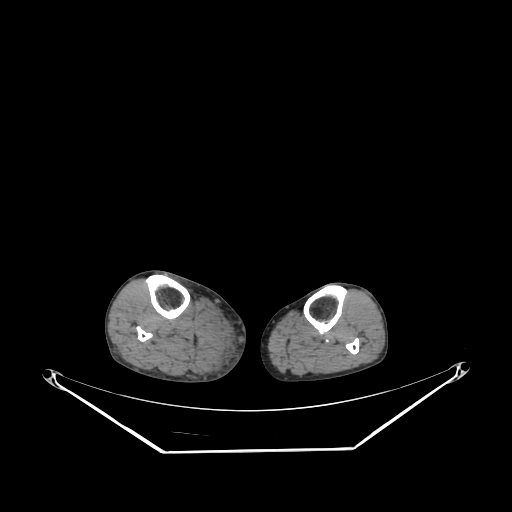
CT of an extremity soft-tissue mass (from a PET/CT study), one axial slice; position 147 of 267 along the scan axis; soft-tissue window (W 400 / L 40 HU); 3.75 mm slice thickness; 512 × 512 image matrix, field of view 500 × 500 mm. Male patient. From the clinical record (not read from this slice): histological type: pleiomorphic liposarcoma; grade: high; site of the primary tumour: right calf.
Outlined on this slice (expert contour drawn on MRI and transferred to this co-registered scan by the dataset authors):
- gross tumour volume including surrounding oedema: bounding box <219,317,231,350> (left, top, right, bottom; pixels)